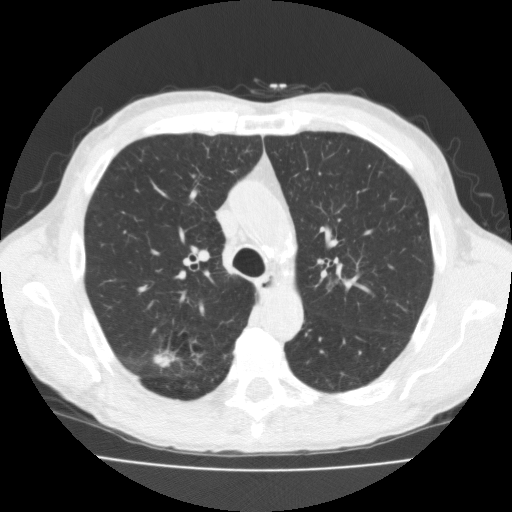
Low-dose screening chest CT, one axial slice; slice 123 of 181 in the series (ordered by position); 120 kVp; lung window (W 1500 / L -600 HU); 2 mm slice thickness; 512 × 512 image matrix, field of view 350 × 350 mm.
Annotated regions visible in this slice (expert manual segmentation):
- lesion 1 (tumor, upper lobe of right lung): bounding box <154,350,175,367> (left, top, right, bottom; pixels)